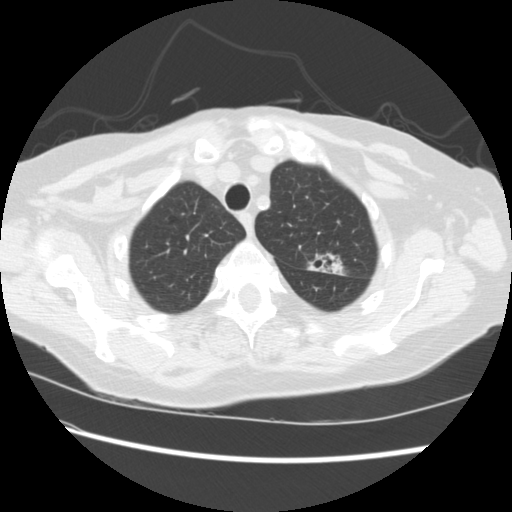
Low-dose screening chest CT, one axial slice. Position 183 of 224 along the scan axis. Lung window (W 1500 / L -600 HU). 2.5 mm slice thickness. 512 × 512 image matrix.
Outlined on this slice (outlined manually by an expert reader):
- lesion 1 (tumor, upper lobe of left lung): bounding box [x1, y1, x2, y2] px = [329, 260, 344, 275]